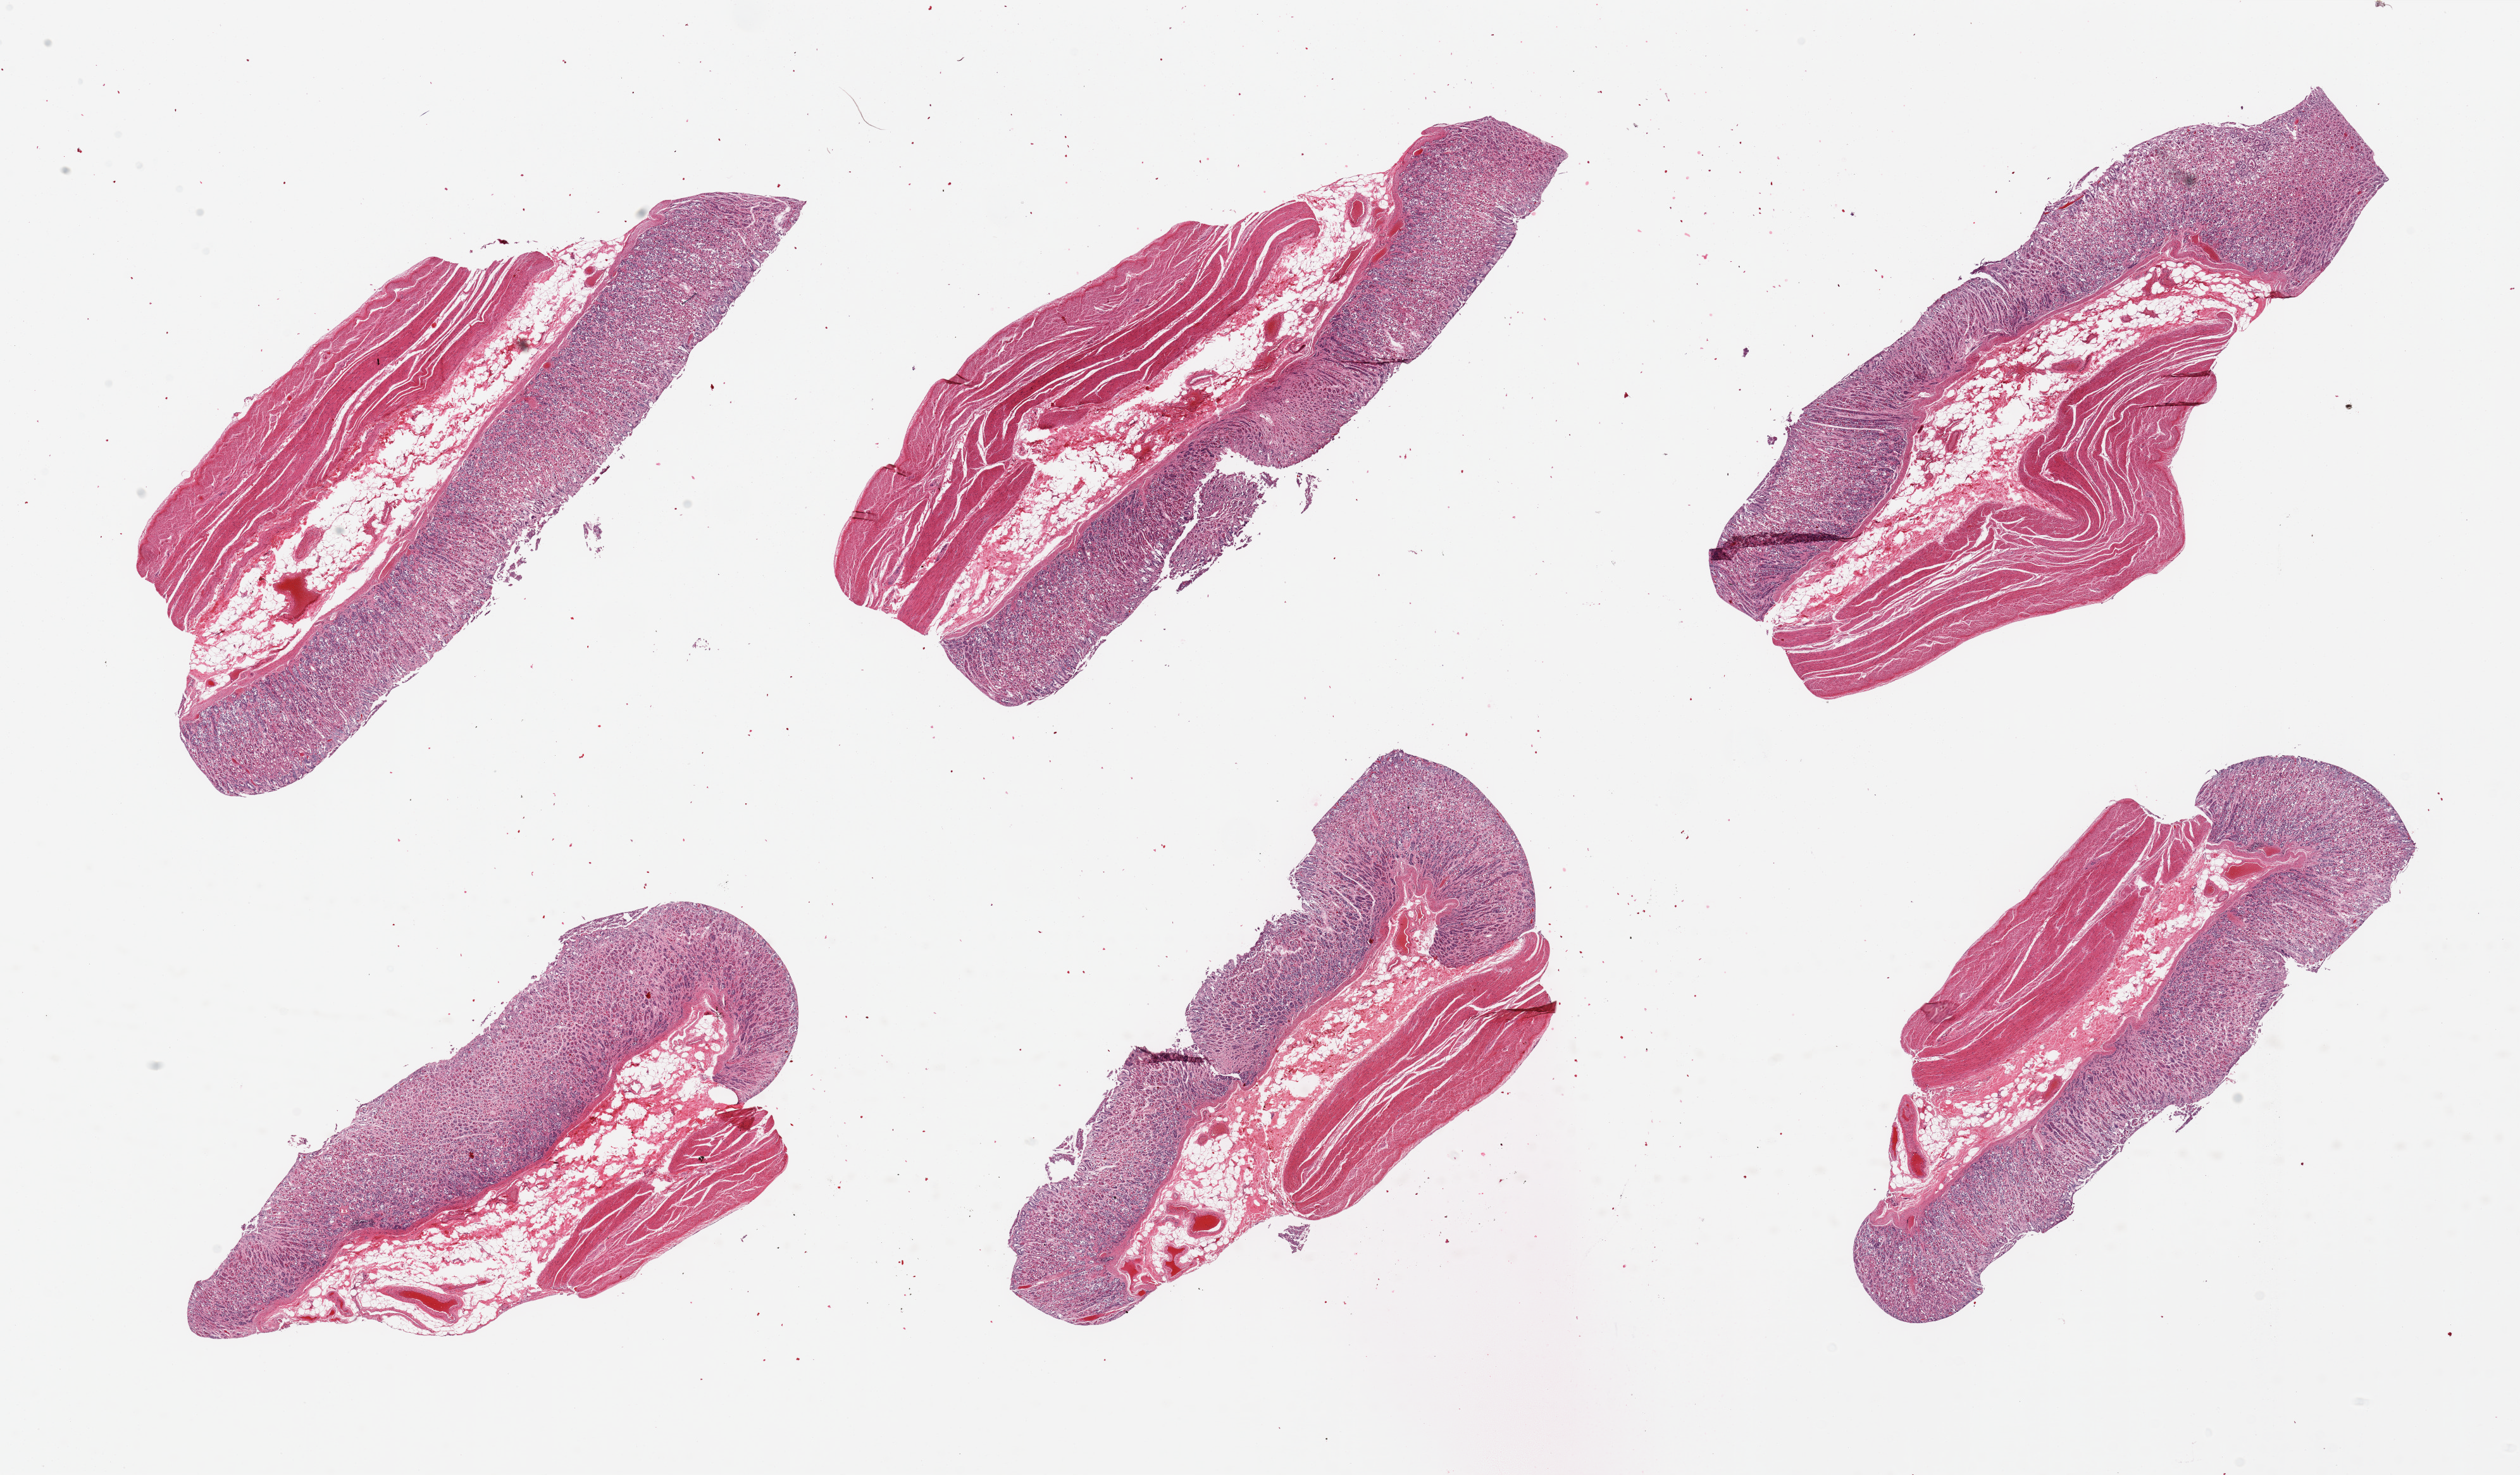
Digitized haematoxylin and eosin-stained section, brightfield, low-resolution overview of the scanned area, about 31.5 x 18.4 mm (slide scanned at 20x). PAXgene-fixed, paraffin-embedded tissue. Sampled site (target tissue): stomach. Donor tissue sample. Donor sex: male.
• review note (as recorded): pieces